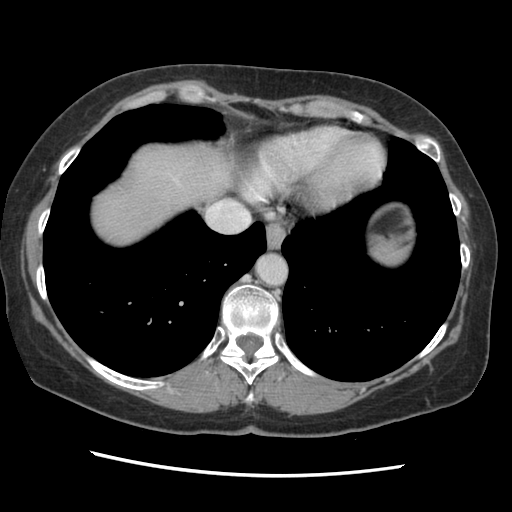
Contrast-enhanced abdominal CT, one axial slice; position 124 of 141 along the scan axis; soft-tissue window (W 400 / L 40 HU); 512 × 512 image matrix, field of view 330 × 330 mm. Female patient, age 61 years. From the clinical record (not read from this slice): diagnosis: colorectal cancer liver metastases, imaged before liver resection; multiple liver metastases: no; largest metastasis: 2.4 cm; disease in both lobes: no.
Outlined on this slice (manually delineated by an expert):
- liver: bounding box (x1, y1, x2, y2) in pixels: (90, 143, 232, 246)
- planned liver remnant (the part of the liver to remain after resection): (90, 143, 232, 246)